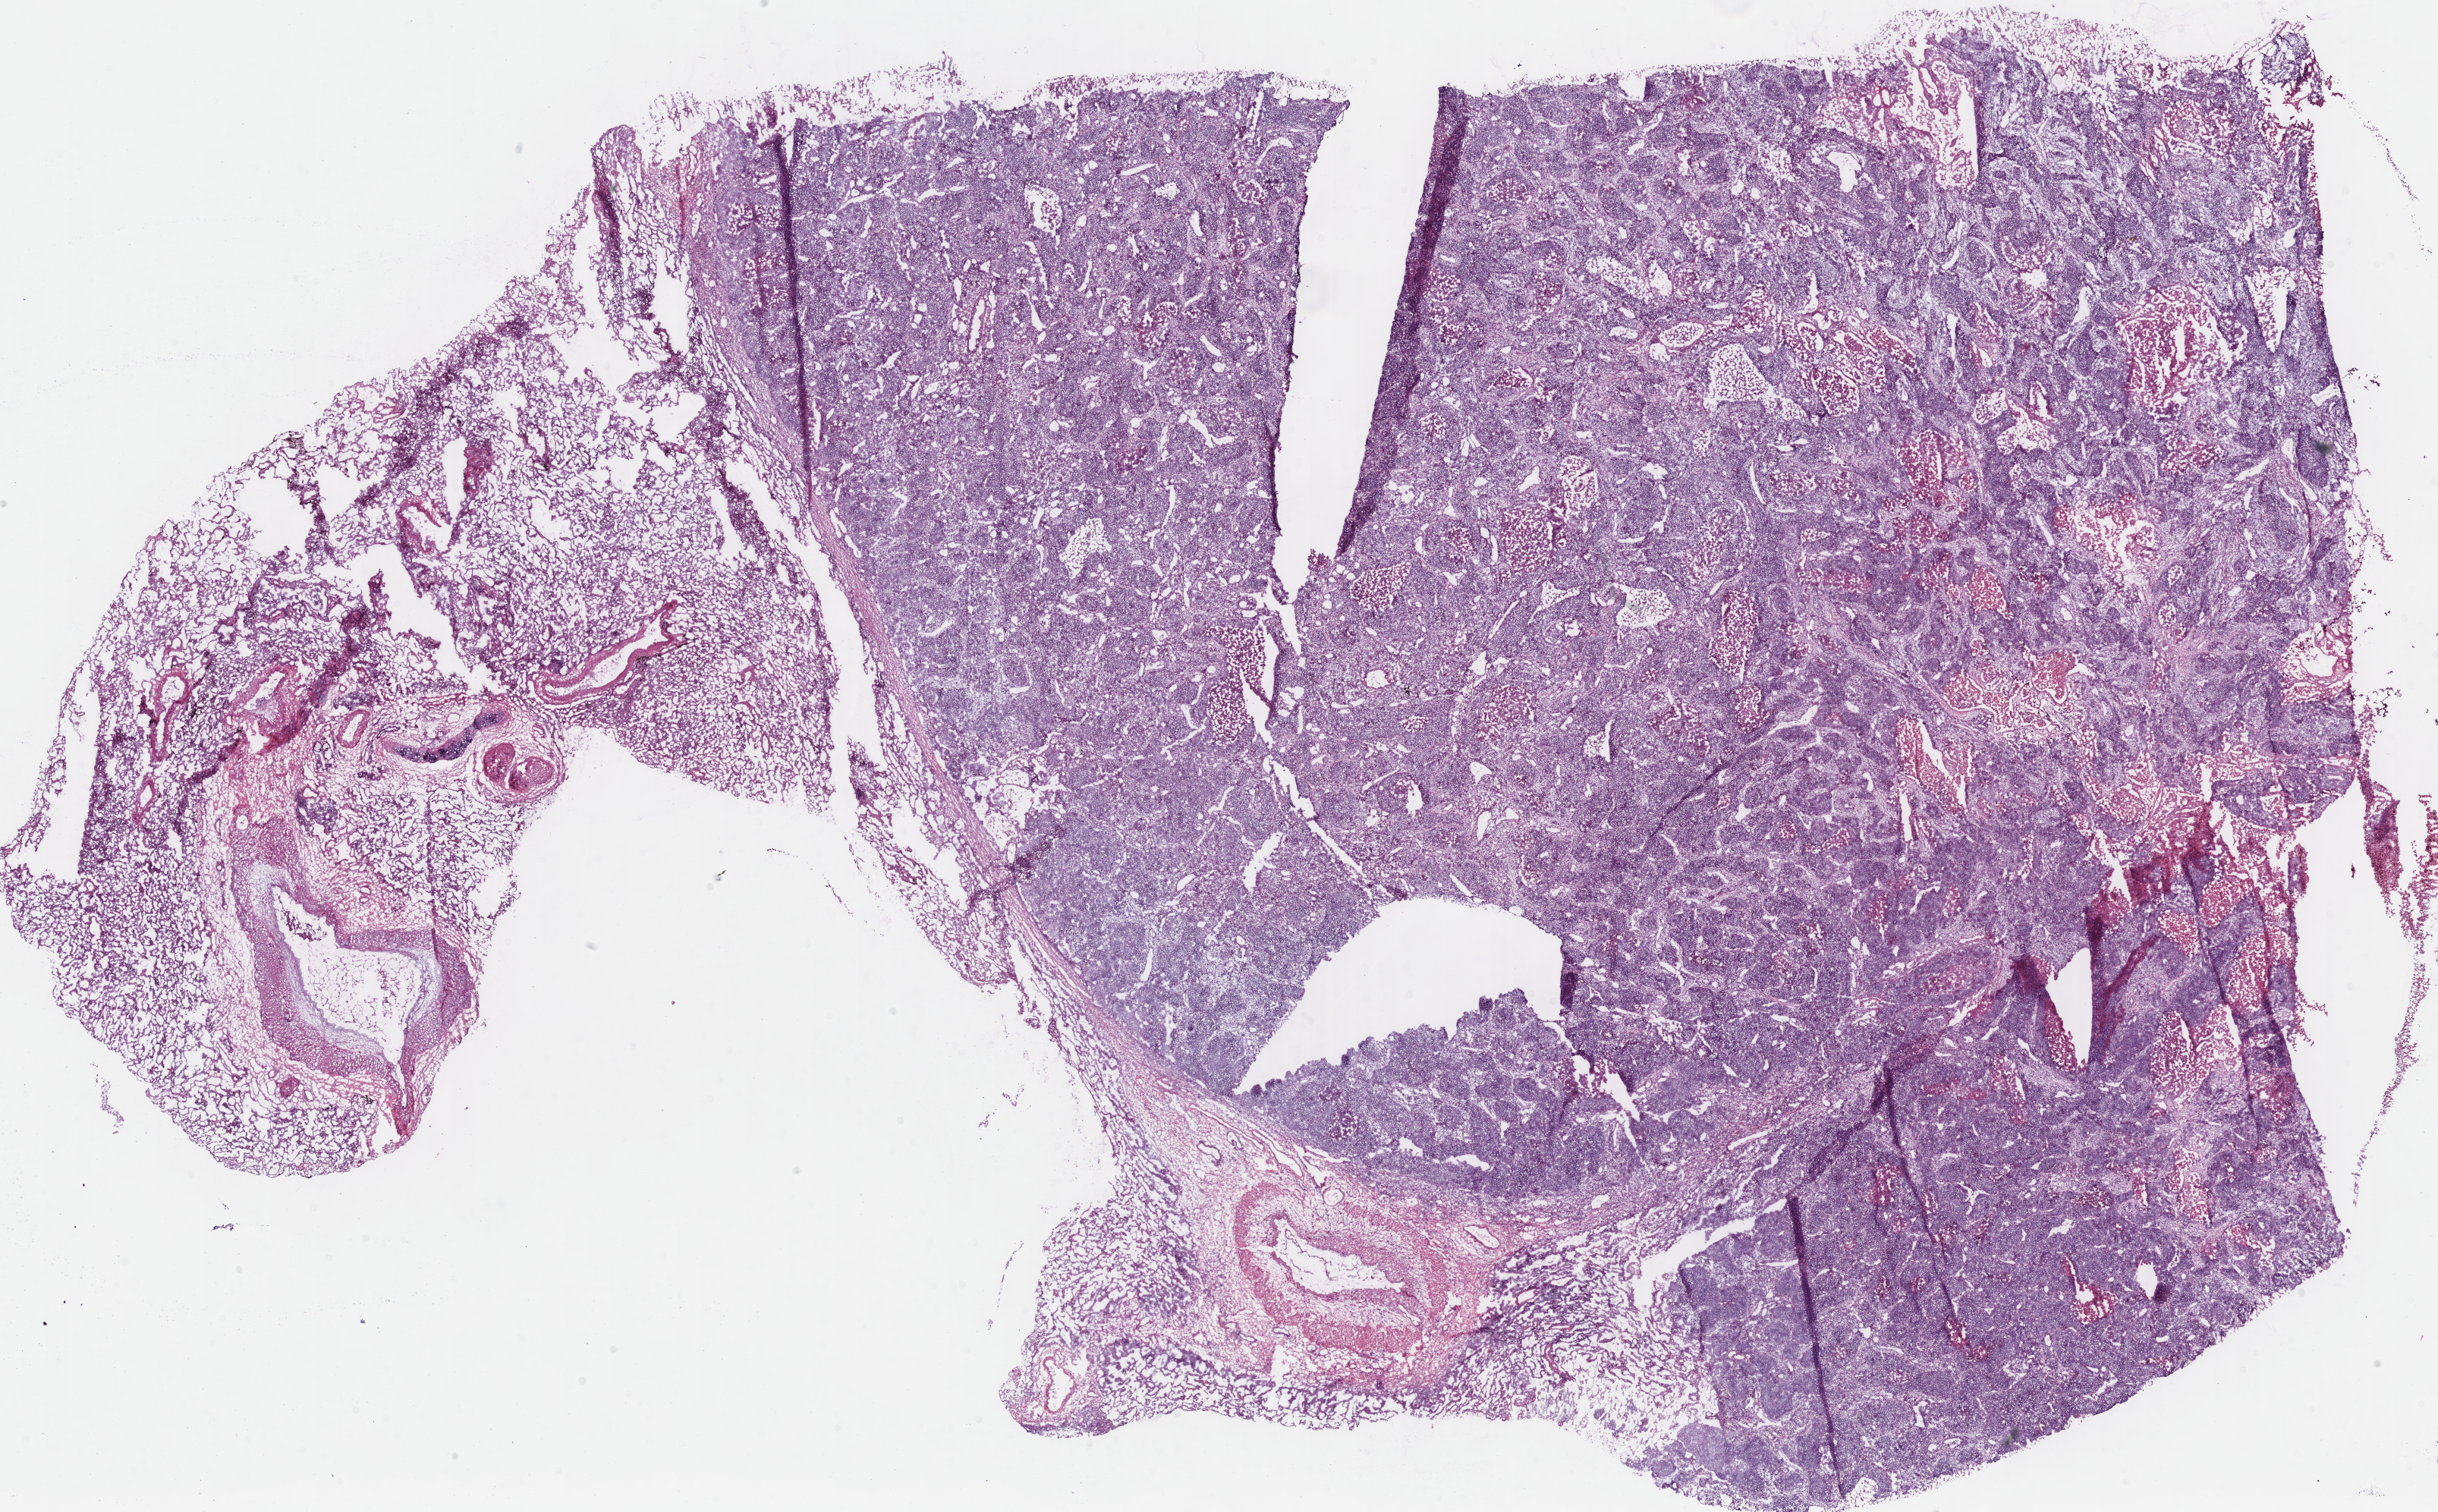
H&E-stained whole-slide image, a low-resolution overview of the entire scanned area, about 25.3 x 15.7 mm (slide scanned at 40x). Frozen section. Lung, primary tumour sample. Male patient; age at initial diagnosis 73 years.
Diagnosis: Squamous cell carcinoma, NOS (upper lobe, lung).